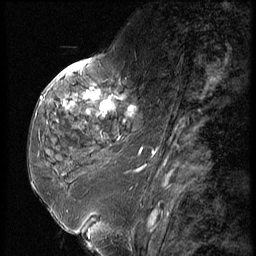
Breast MRI (dynamic contrast-enhanced), one sagittal slice; position 22 of 56 along the scan axis; dynamic contrast-enhanced series, image 2 of 3 at this slice position (ordered by acquisition); 1.5 T; TE 4.2 ms, TR 9 ms; 256 × 256 image matrix, field of view 180 × 180 mm. Patient: female, 59 years. Case-level facts recorded for this patient, not image findings: setting: breast cancer imaged before/during neoadjuvant chemotherapy; receptor status: HER2-positive.
Annotated regions visible in this slice (semi-automatically segmented with operator editing):
- analysis volume of interest (the breast-tissue region the enhancement analysis was run in; not a lesion): bounding box [x1, y1, x2, y2] px = [44, 66, 151, 135]
- tumour enhancement mask (voxels above the 140 % enhancement threshold inside the analysis volume of interest): [63, 88, 134, 116]